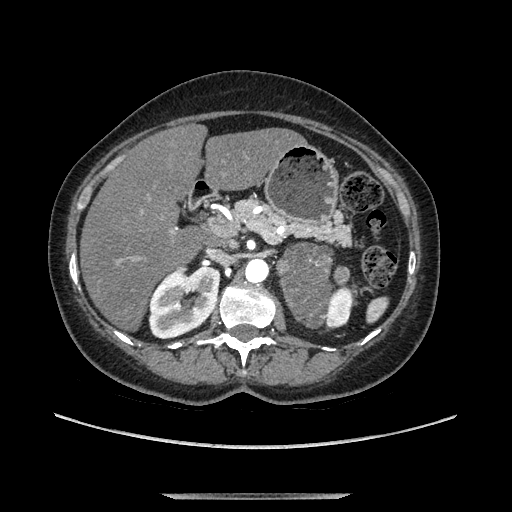
Contrast-enhanced abdominal CT, one axial slice; position 68 of 169 along the scan axis; soft-tissue window (W 400 / L 40 HU); 1.25 mm slice thickness; 512 × 512 image matrix, field of view 400 × 400 mm. Female patient. From the clinical record (not read from this slice): diagnosis: adrenocortical carcinoma; tumour side: left adrenal; tumour size at pathology: 9 cm; Ki-67 index: 2 %; stage (as recorded): 3.
Outlined on this slice (semi-automatically segmented with operator editing):
- mass: bounding box (x1, y1, x2, y2) in pixels: (280, 246, 332, 325)